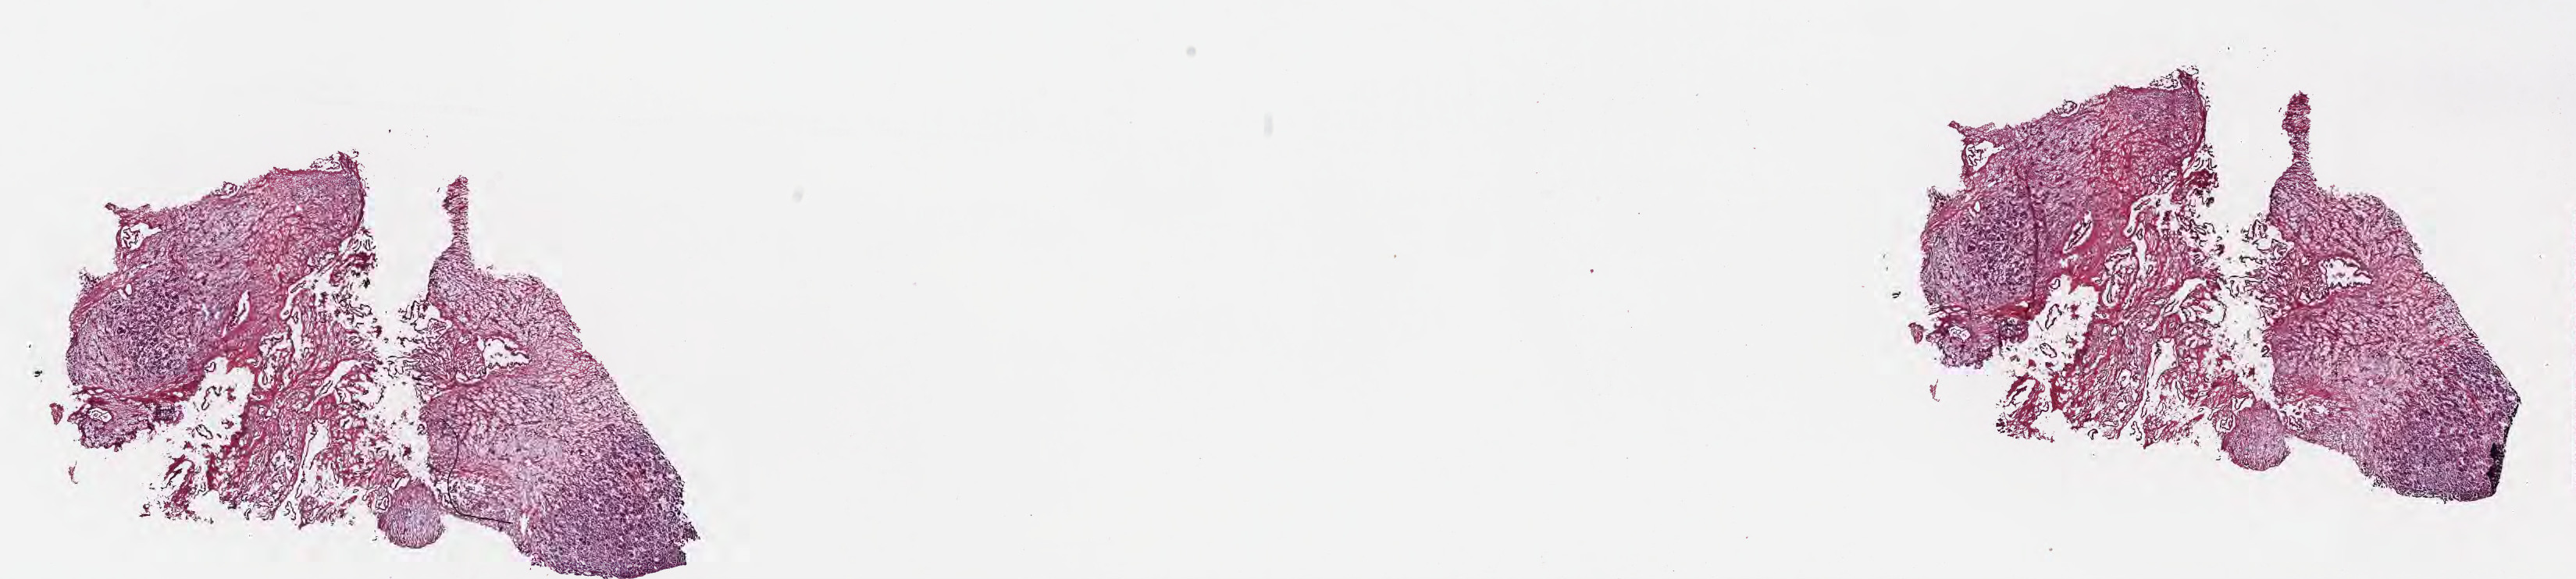
Digitized H&E-stained section, whole scanned area (about 26.7 x 6.0 mm) shown as a low-resolution overview, frozen section (tissue freezing medium), primary tumor, site: head of pancreas. Patient: female, age at initial diagnosis 60 years. Tumor grade: G2 (moderately differentiated). Pathologist review of this section (percent, as recorded): tumor cells 25%, tumor nuclei 35%, stromal cells 55%, necrosis 0%, normal cells 20%. Infiltration values recorded for this section: lymphocyte infiltration 0%, monocyte infiltration 0%, neutrophil infiltration 0%.
Diagnosis: Infiltrating duct carcinoma, NOS. Section: top of the tissue portion. AJCC pathologic stage: Stage III.